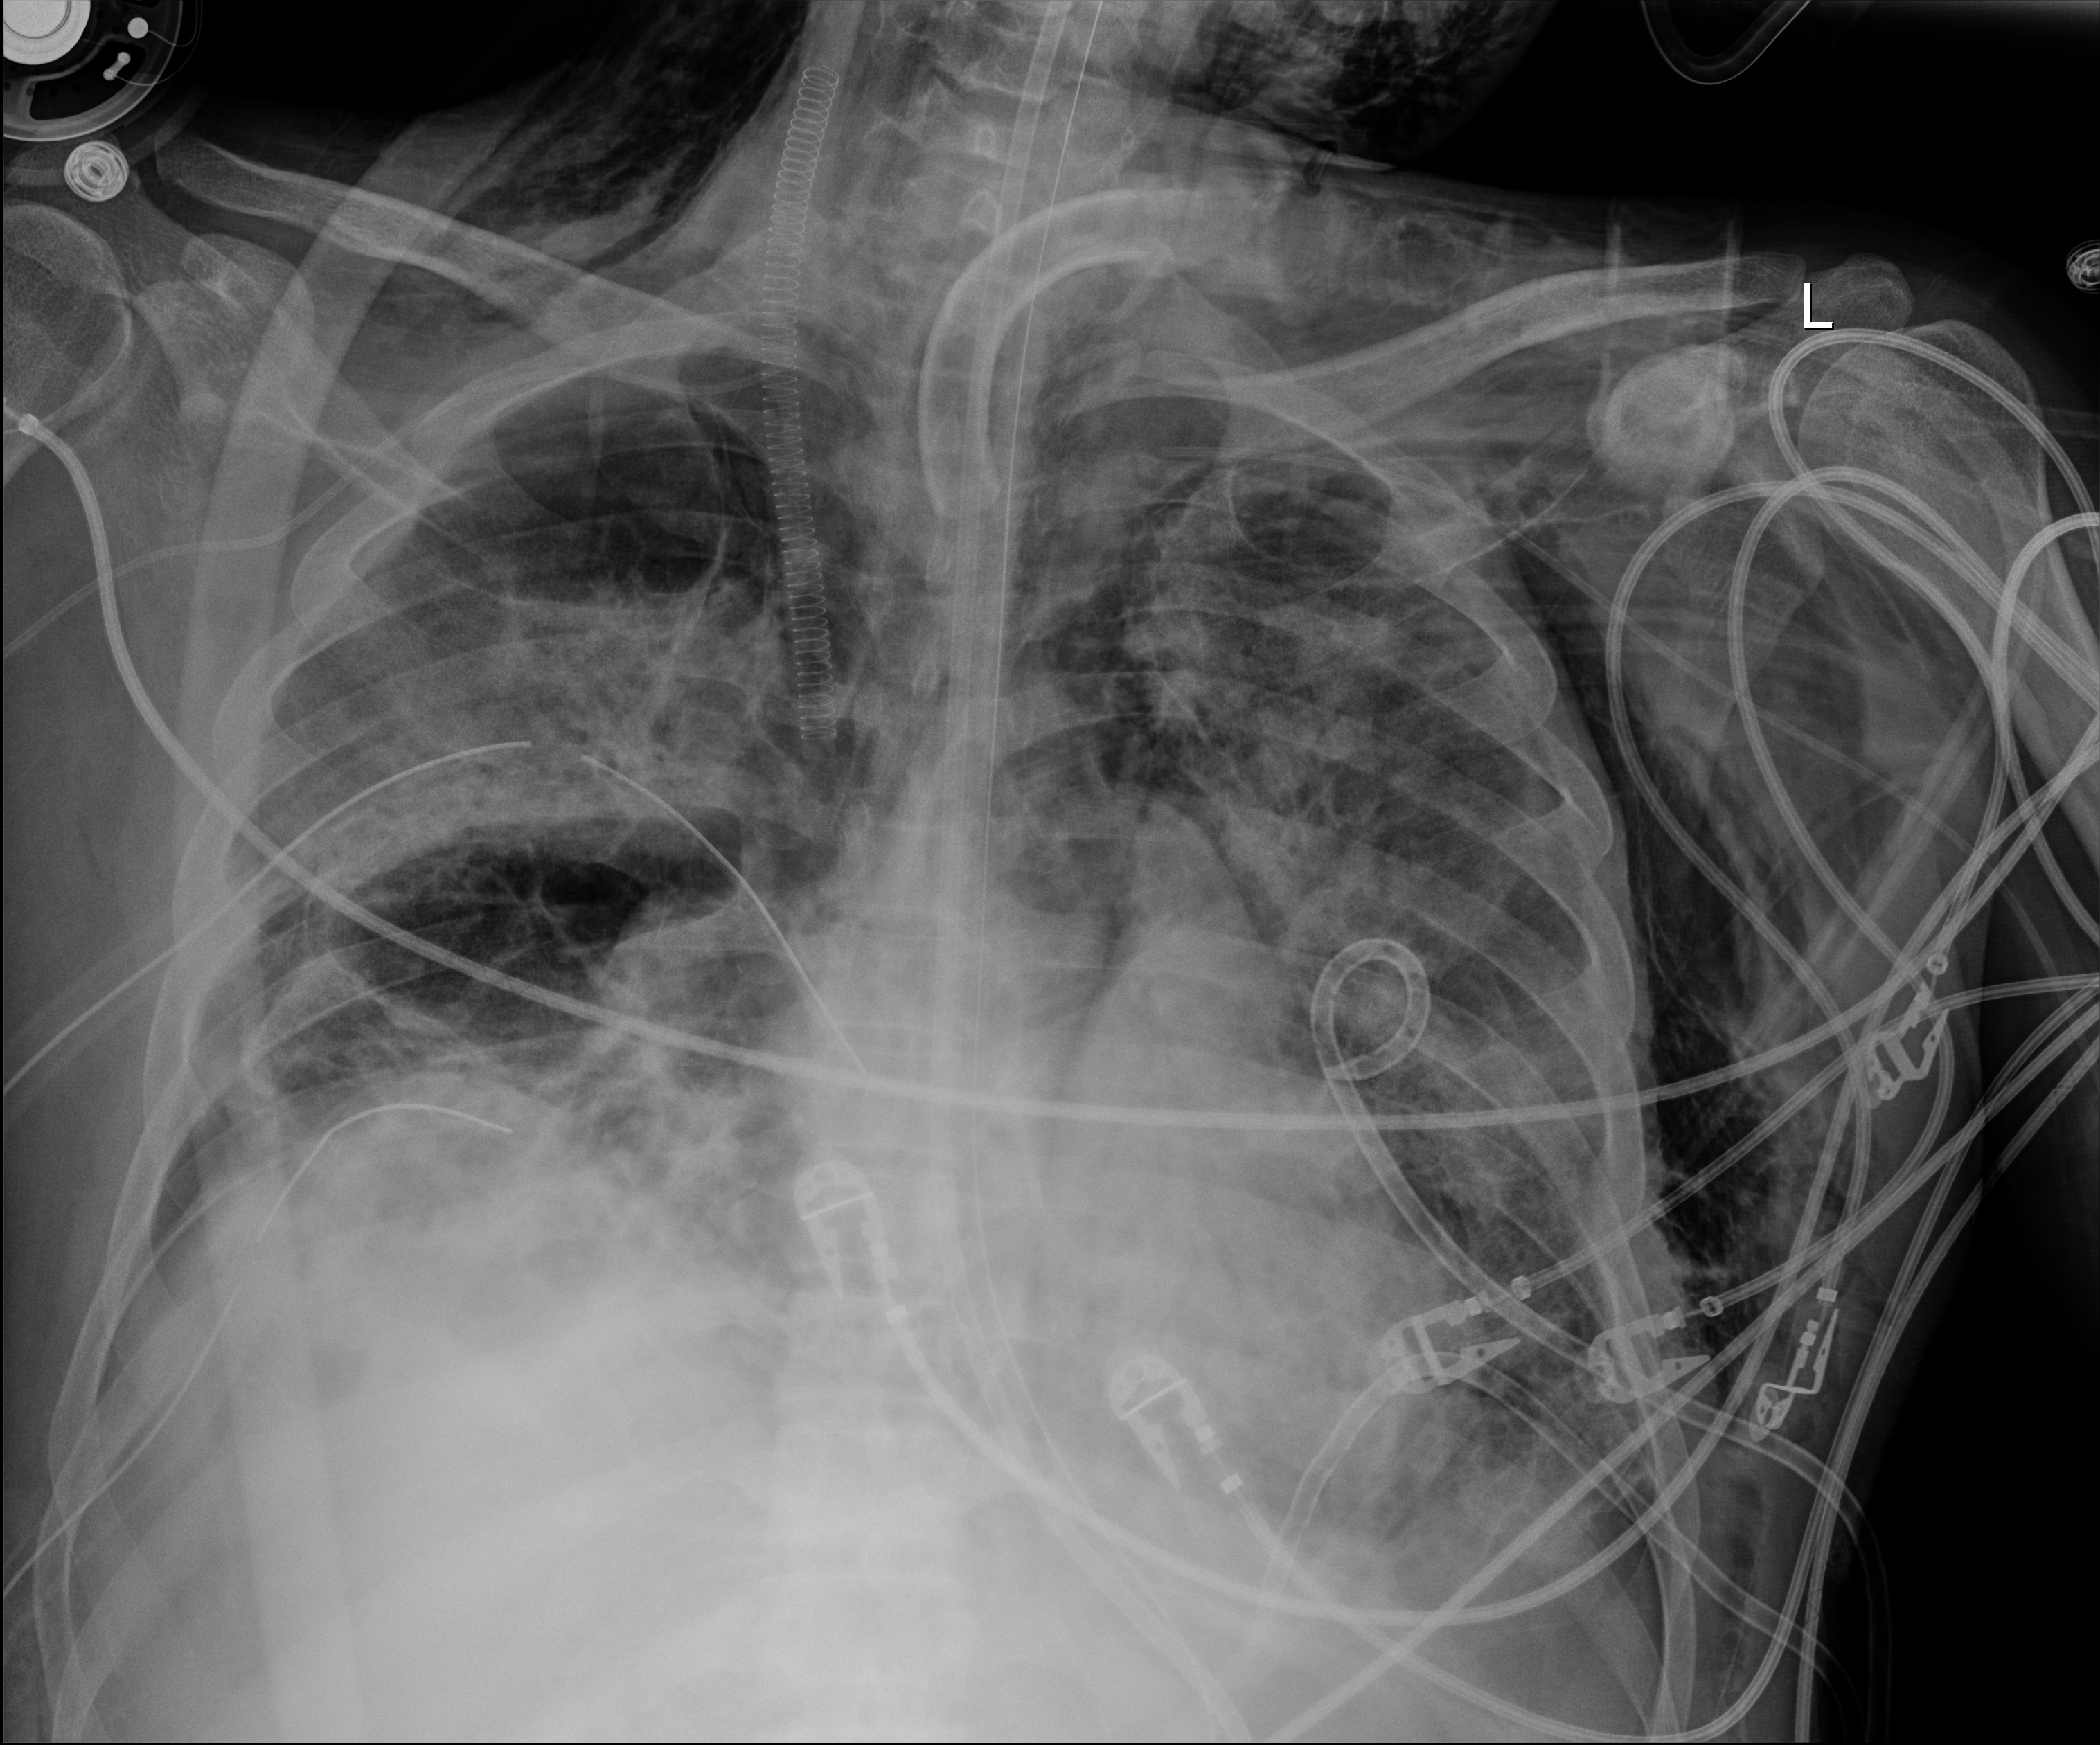
Bedside chest radiograph (digital radiography); anteroposterior (AP) projection. Patient hospitalised with COVID-19, aged 18–59 years.
From the hospital-stay record, not from the radiograph (when in the stay this image was taken is not recorded): length of hospital stay: 60 days; chronic kidney disease (admission record): no; mechanically ventilated during this hospital stay: yes.